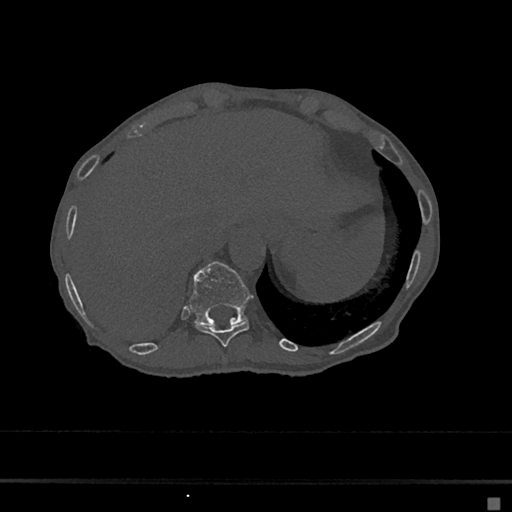
CT including the spine, one axial slice; slice 203 of 797 in the series (ordered by position); reconstruction kernel Br40s/3; bone window (W 1800 / L 400 HU); 512 × 512 image matrix. Female patient, age 68 years. Case-level facts recorded for this patient, not image findings: primary cancer: renal.
Outlined on this slice (semi-automatically segmented with operator editing):
- T10 vertebra: bounding box (x1, y1, x2, y2) in pixels: (195, 320, 249, 347)
- T11 vertebra: (189, 262, 252, 325)